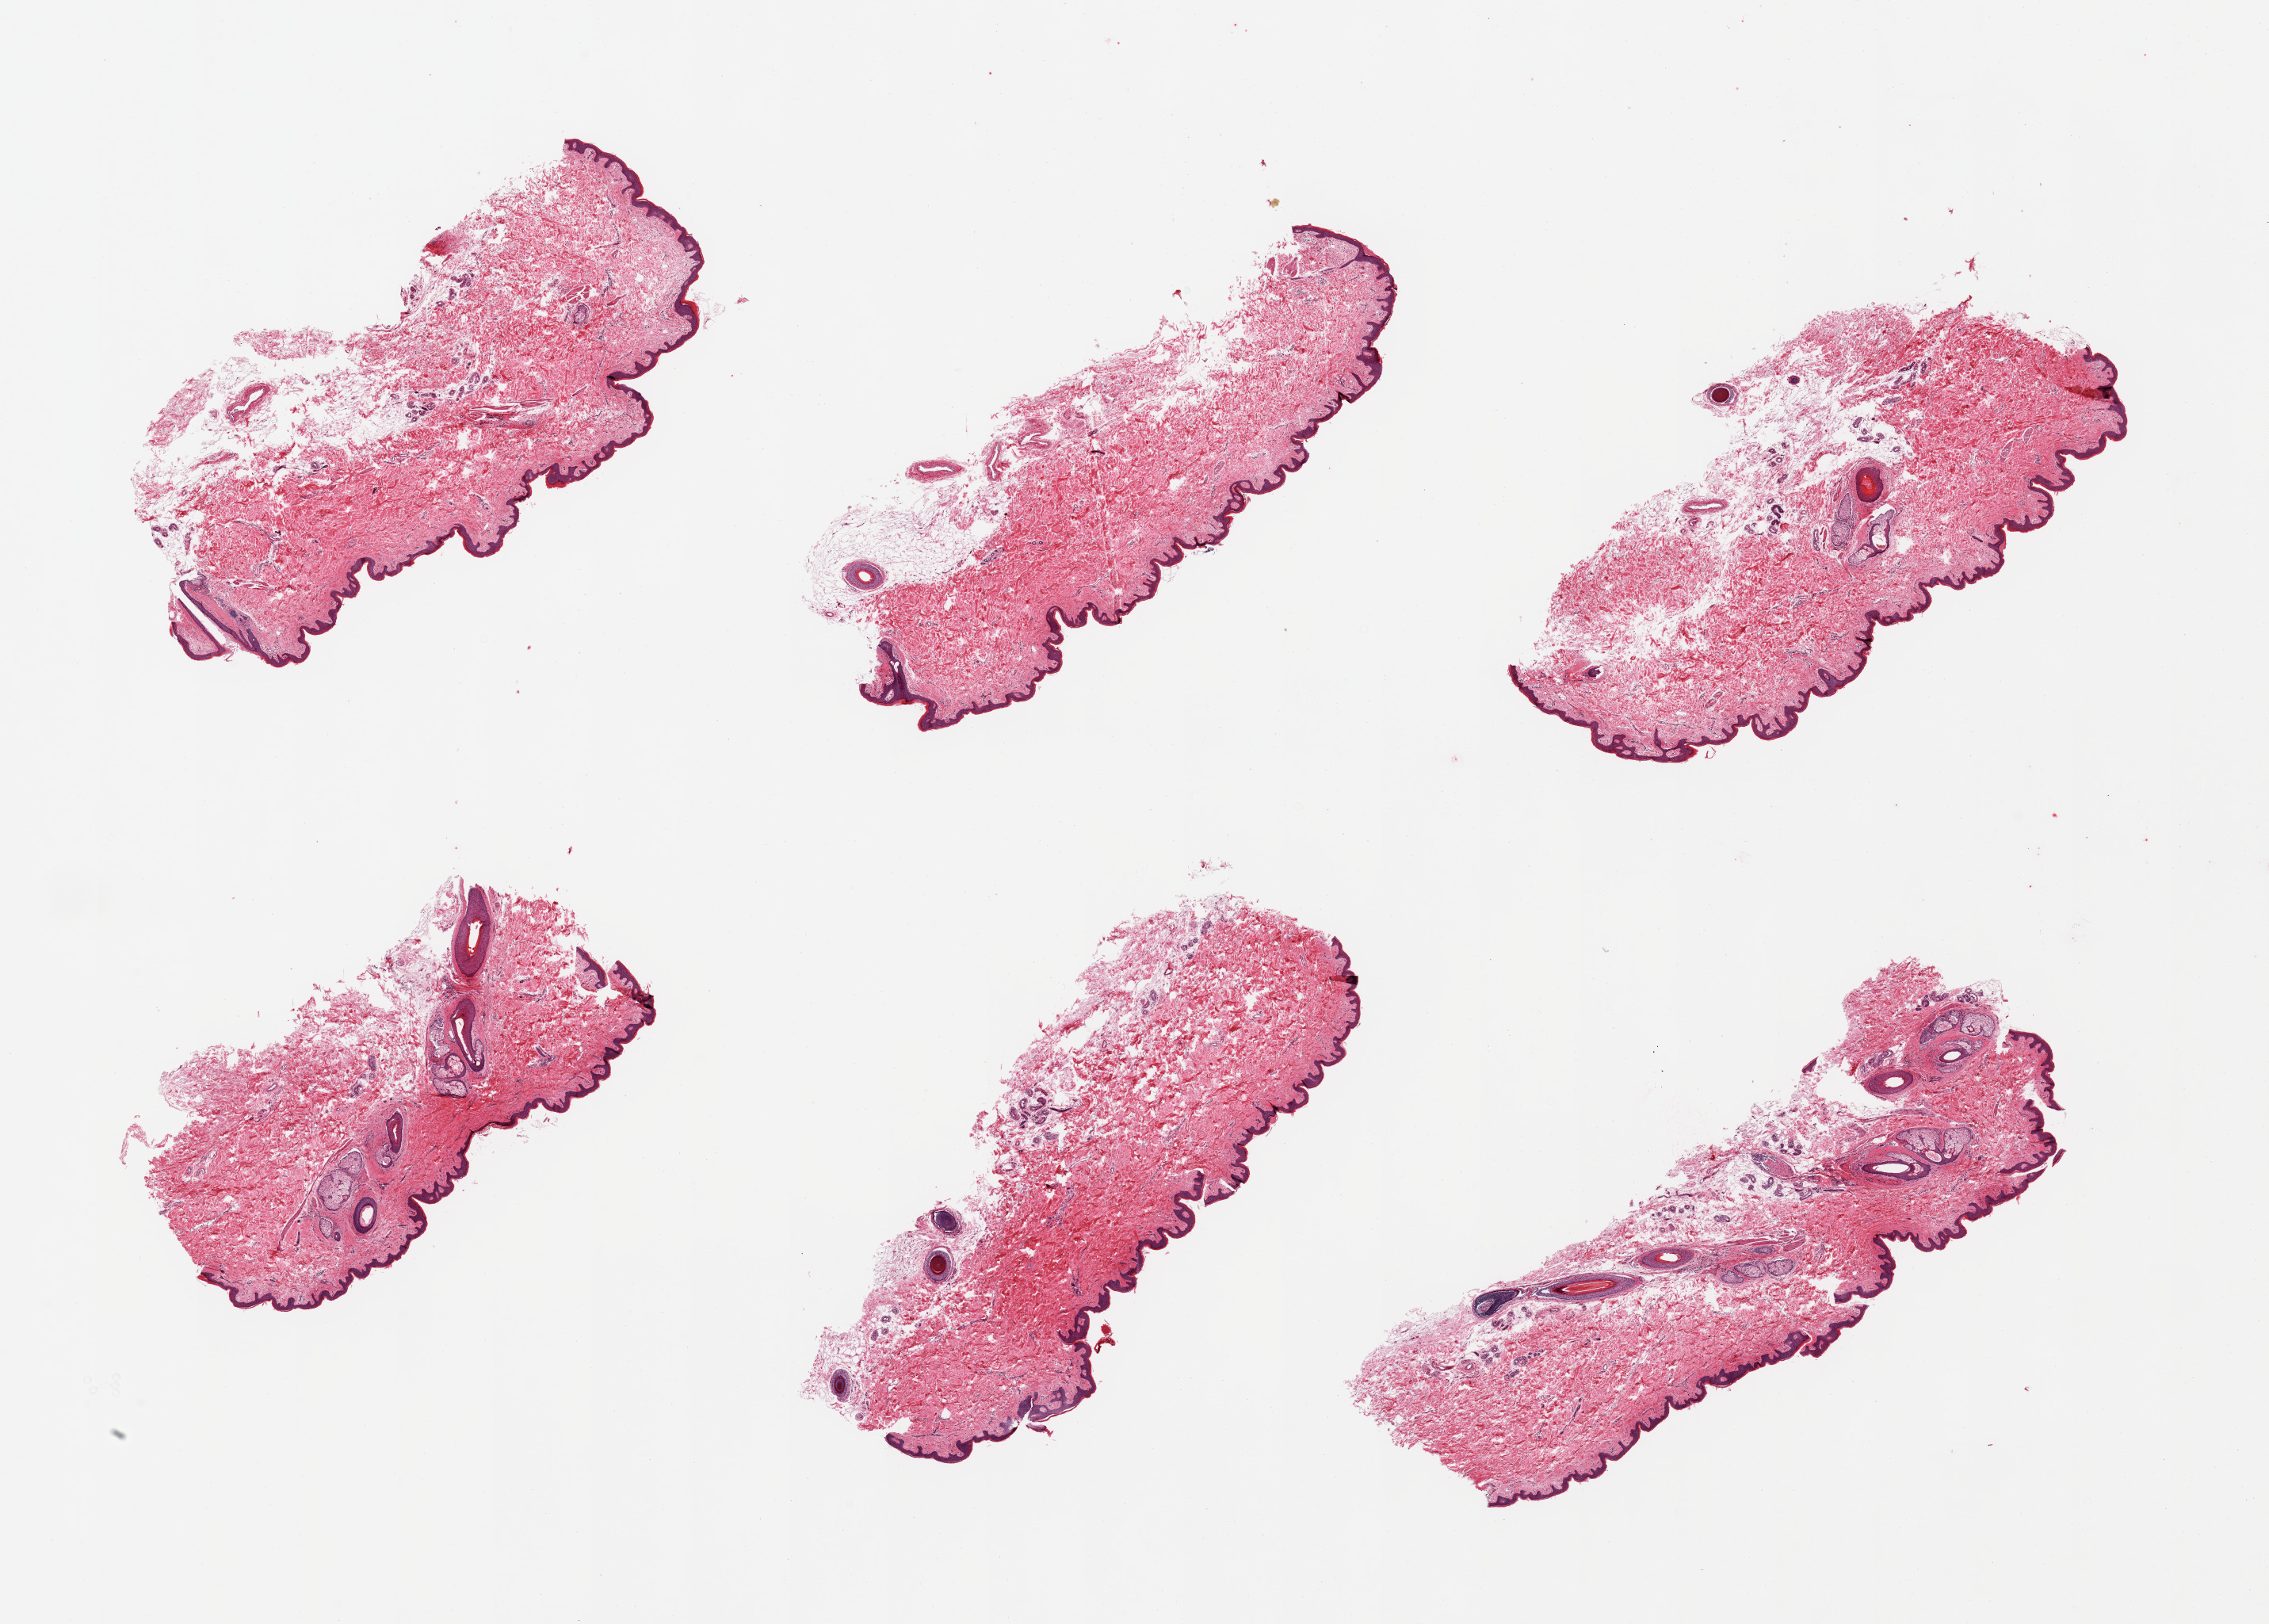
Digitized H&E-stained section — low-resolution overview of the scanned area, about 22.6 x 16.2 mm, PAXgene-fixed paraffin-embedded (PFPE) section, sampled site (target tissue): skin of suprapubic region, tissue donor sample. Male donor.
Review note (as recorded): 6 pieces, trace dermal fat, squamous epithelium is ~60 microns.